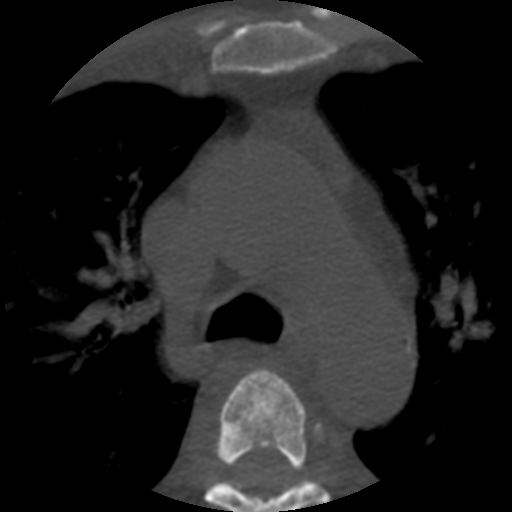
CT including the spine, one axial slice; slice 394 of 508 in the series (ordered by position); reconstruction kernel STANDARD; 120 kVp; bone window (W 1800 / L 400 HU); 512 × 512 image matrix. Patient age 57 years. Case-level facts recorded for this patient, not image findings: primary cancer: prostate.
Structures marked on this image (semi-automatic segmentation, software-assisted and operator-edited):
- T3 vertebra: bounding box (x1, y1, x2, y2) in pixels: (244, 369, 292, 392)
- T4 vertebra: (204, 376, 329, 512)
- T5 vertebra: (216, 477, 301, 492)